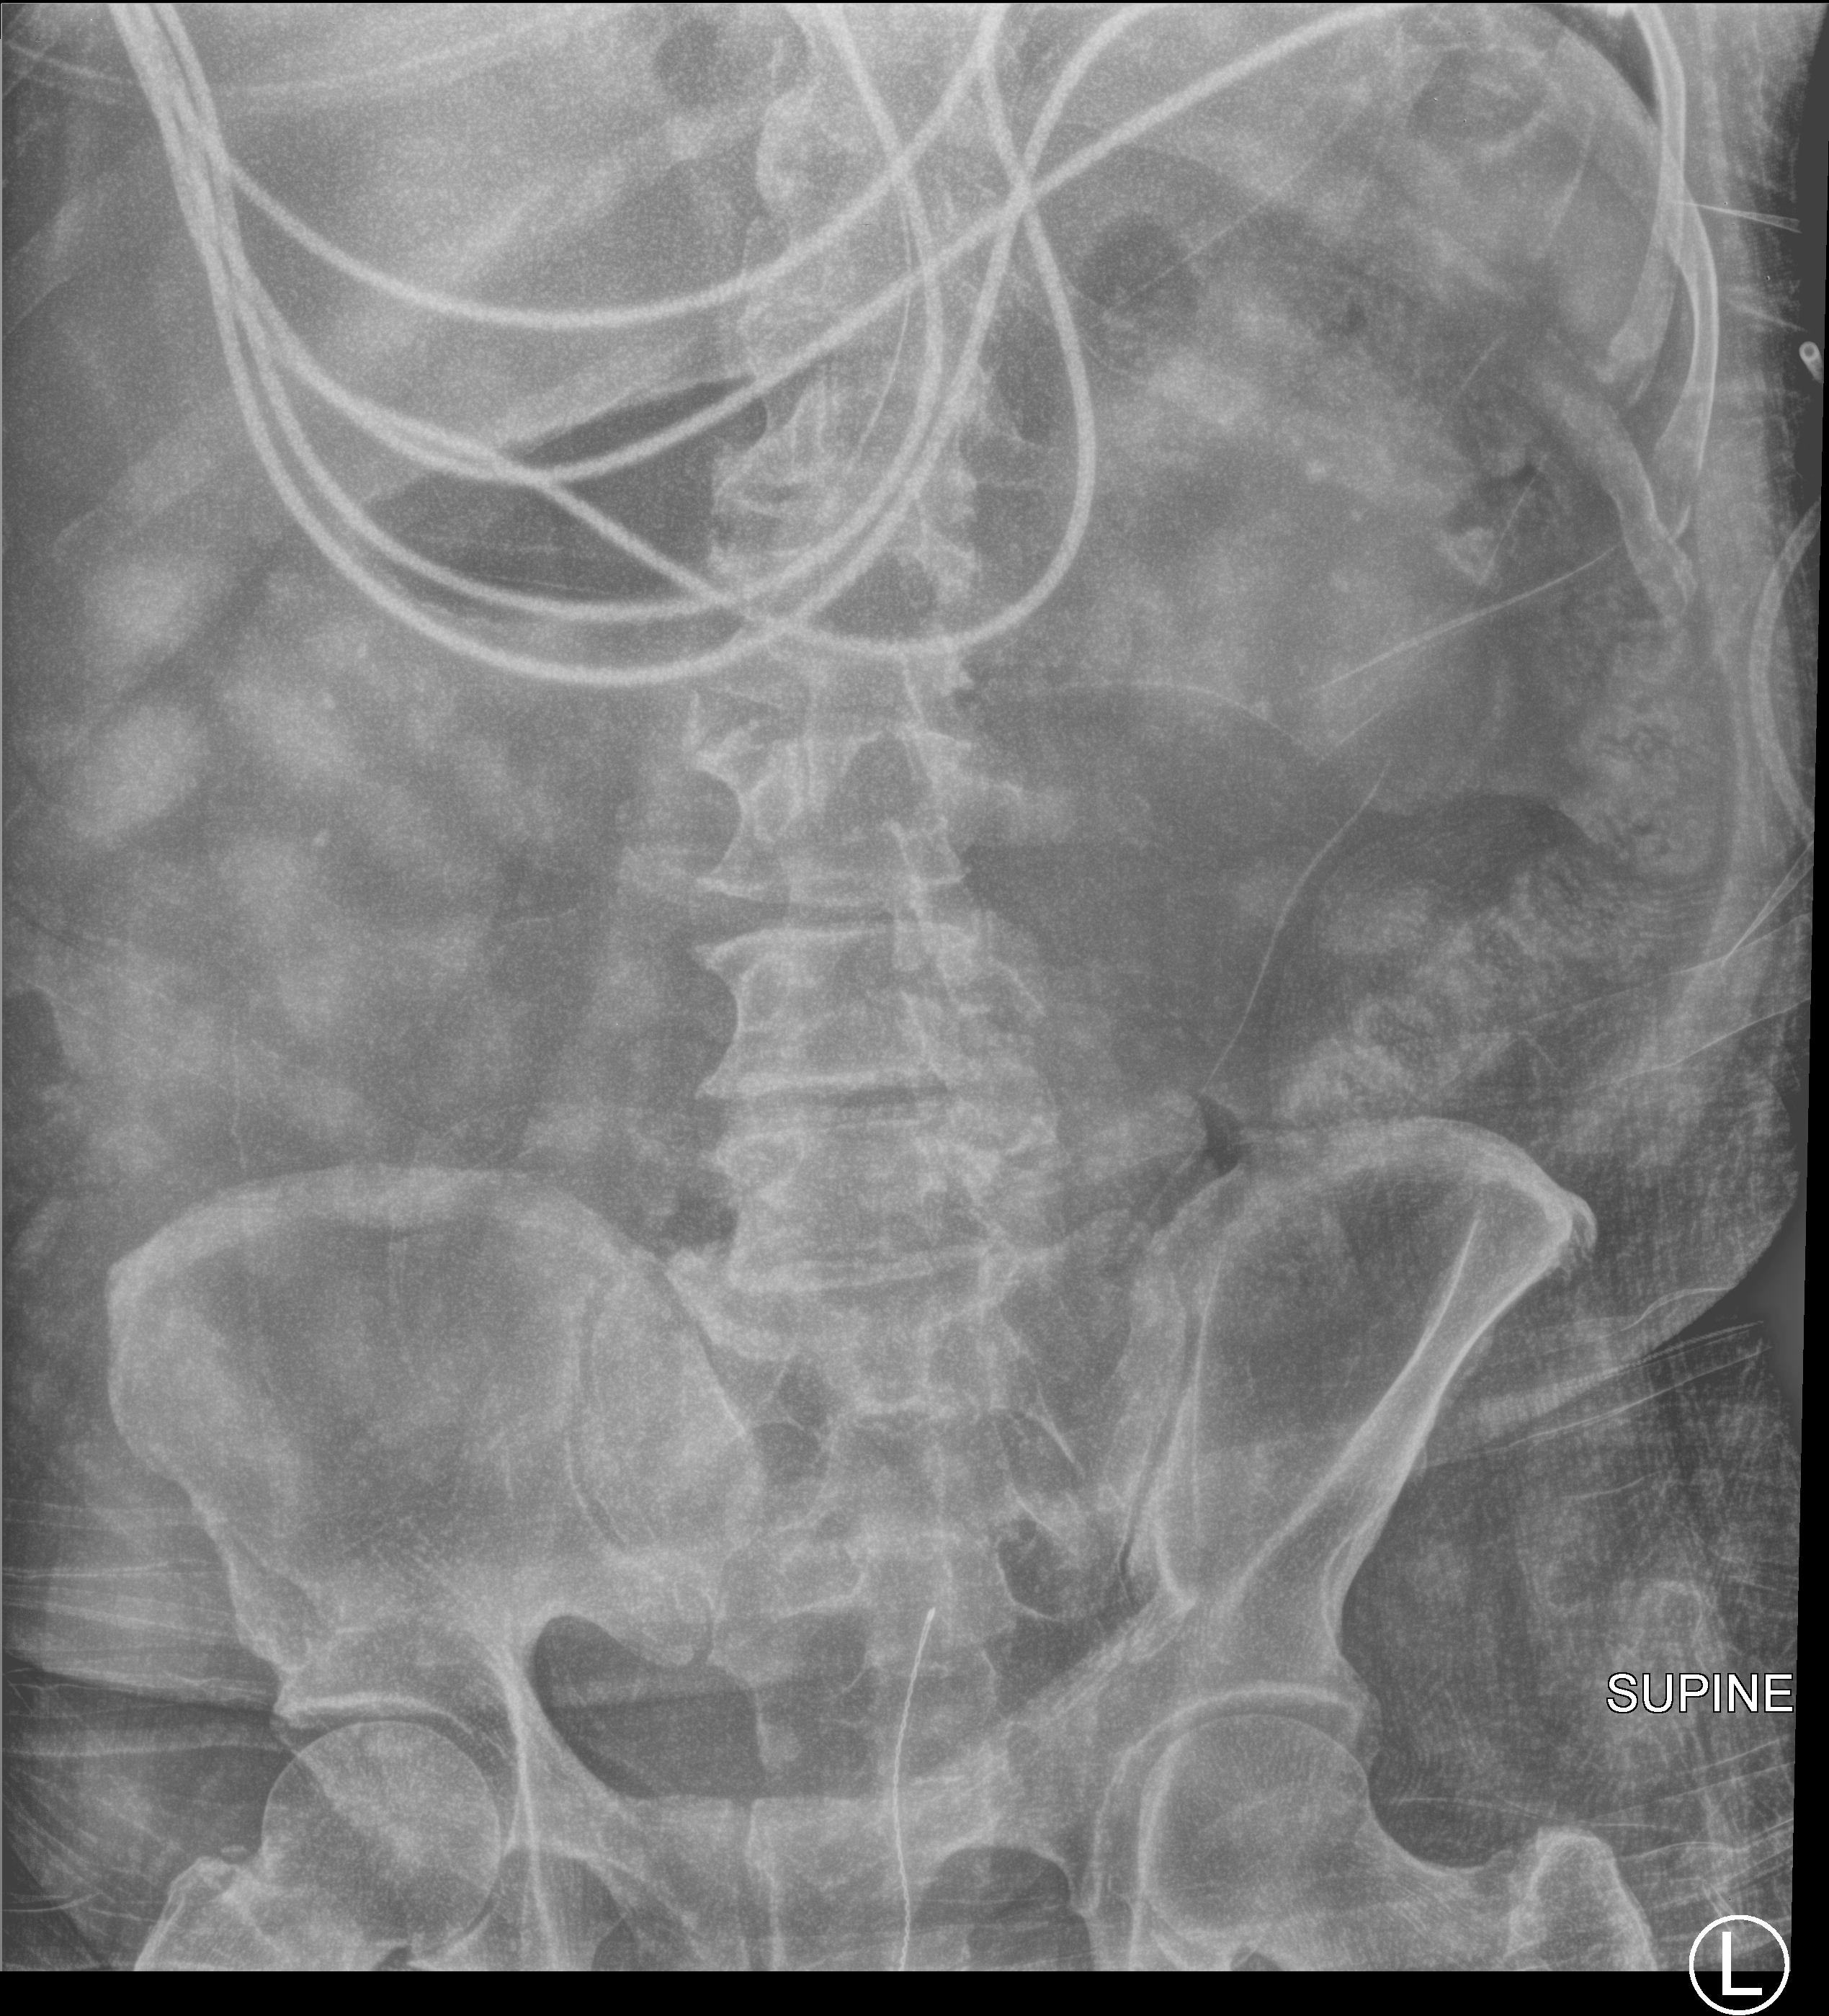
Portable abdomen radiograph, anteroposterior (AP) projection. Patient hospitalised with COVID-19; male, aged 60–74 years.
From the hospital-stay record, not from the radiograph (when in the stay this image was taken is not recorded): mechanically ventilated during this hospital stay: yes; admitted to intensive care during this hospital stay: yes.